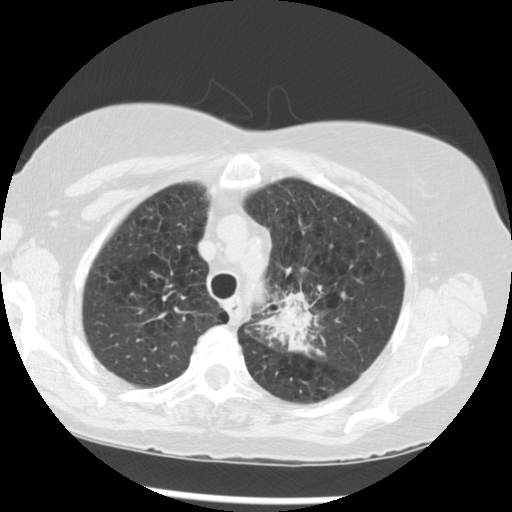
Low-dose screening chest CT, one axial slice; reconstruction kernel STANDARD; 120 kVp; lung window (W 1500 / L -600 HU); 2.5 mm slice thickness; 512 × 512 image matrix, field of view 330 × 330 mm.
Outlined on this slice (expert manual segmentation):
- lesion 1 (tumor, upper lobe of left lung): bounding box (x1, y1, x2, y2) in pixels: (251, 292, 324, 357)